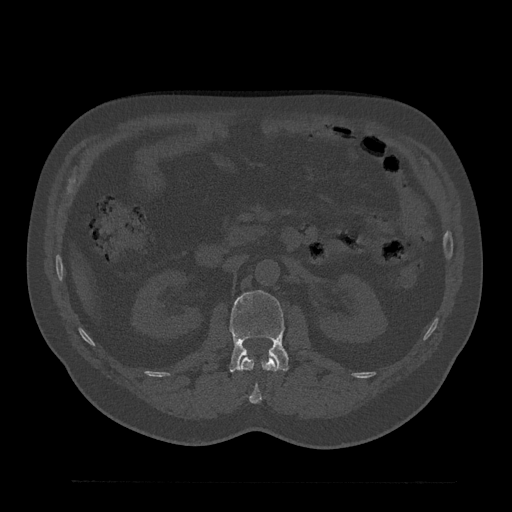
CT including the spine, one axial slice. Position 123 of 797 along the scan axis. Bone window (W 1800 / L 400 HU). 0.5 mm slice thickness. 512 × 512 image matrix, field of view 430 × 430 mm. Male patient, age 61 years. Case-level facts recorded for this patient, not image findings: primary cancer: prostate.
Structures marked on this image (semi-automatically segmented with operator editing):
- L1 vertebra: bounding box <240,356,278,403> (left, top, right, bottom; pixels)
- L2 vertebra: <229,290,289,371>